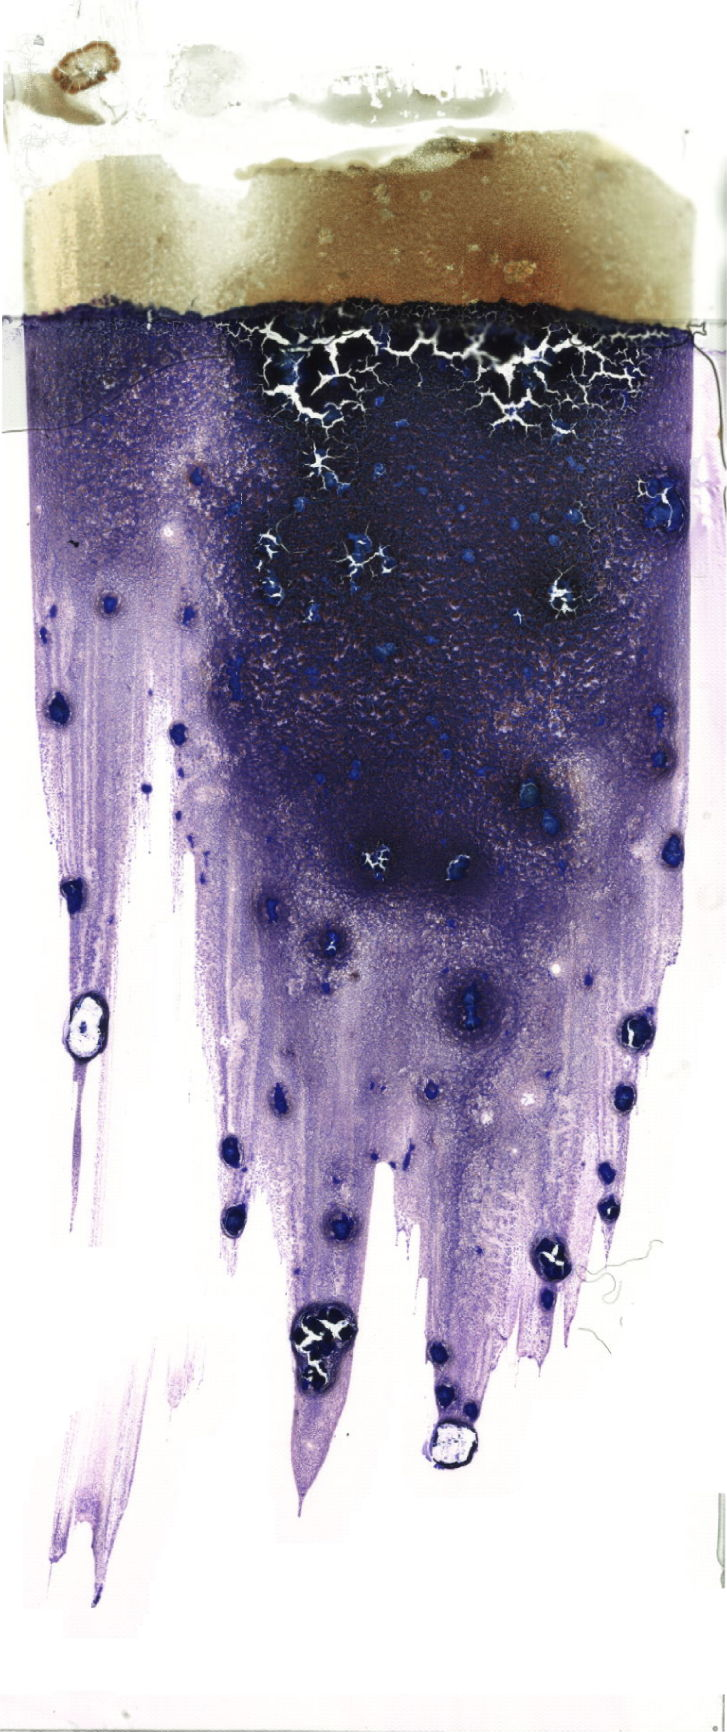
Bone marrow aspirate smear, May-Grünwald–Giemsa stain, whole-slide image — whole scanned area (about 20.6 x 49.1 mm) shown as a low-resolution overview. Female patient.
• diagnosis: Acute Myeloid Leukemia without Maturation